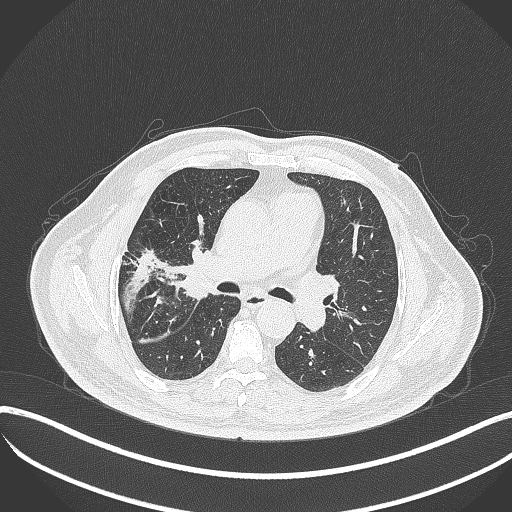
Chest CT, one axial slice; slice 213 of 401 in the series (ordered by position); reconstruction kernel B70f; 120 kVp; lung window (W 1500 / L -600 HU); 1 mm slice thickness; 512 × 512 image matrix, field of view 400 × 400 mm. Patient: male, 72 years. From the clinical record (not read from this slice): clinical TNM (as recorded): T1c N0 M0.
Structures marked on this image (bounding box drawn by a radiologist):
- lung tumour (recorded histology: squamous cell carcinoma): bounding box <169,239,213,304> (left, top, right, bottom; pixels)